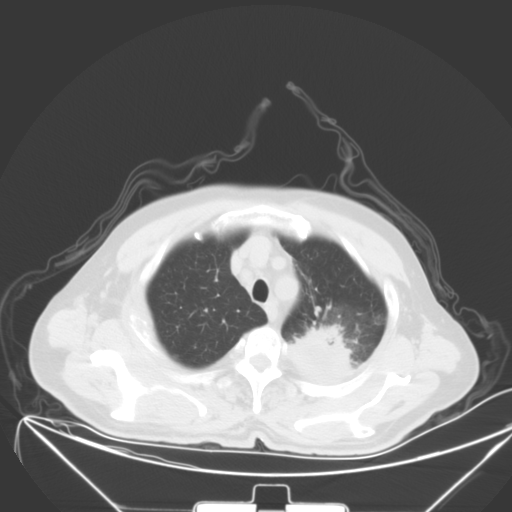
Chest CT, one axial slice. Position 49 of 64 along the scan axis. 120 kVp. Lung window (W 1500 / L -600 HU). 512 × 512 image matrix, field of view 431 × 431 mm. Male patient, age 58 years. From the clinical record (not read from this slice): clinical TNM (as recorded): T2b N3 M1b; histopathological grade: G3.
Outlined on this slice (rectangle marked by the reading radiologist):
- lung tumour (recorded histology: adenocarcinoma): bounding box [x1, y1, x2, y2] px = [285, 319, 355, 389]